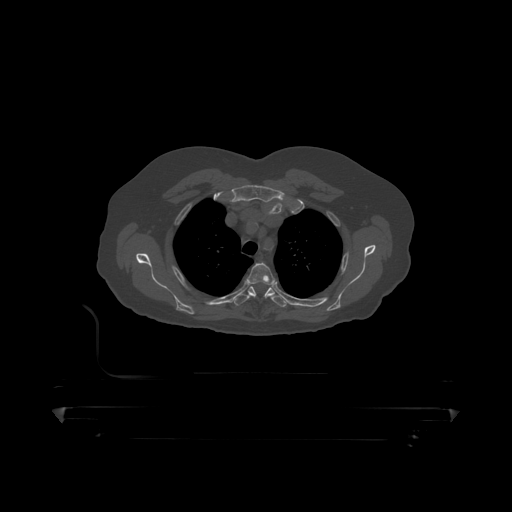
CT including the spine, one axial slice; position 349 of 390 along the scan axis; 120 kVp; bone window (W 1800 / L 400 HU); 1.25 mm slice thickness; 512 × 512 image matrix. Male patient, age 60 years. Case-level facts recorded for this patient, not image findings: primary cancer: prostate.
Outlined on this slice (semi-automatically segmented with operator editing):
- T3 vertebra: bounding box (x1, y1, x2, y2) in pixels: (247, 263, 276, 286)
- T4 vertebra: (234, 286, 287, 307)